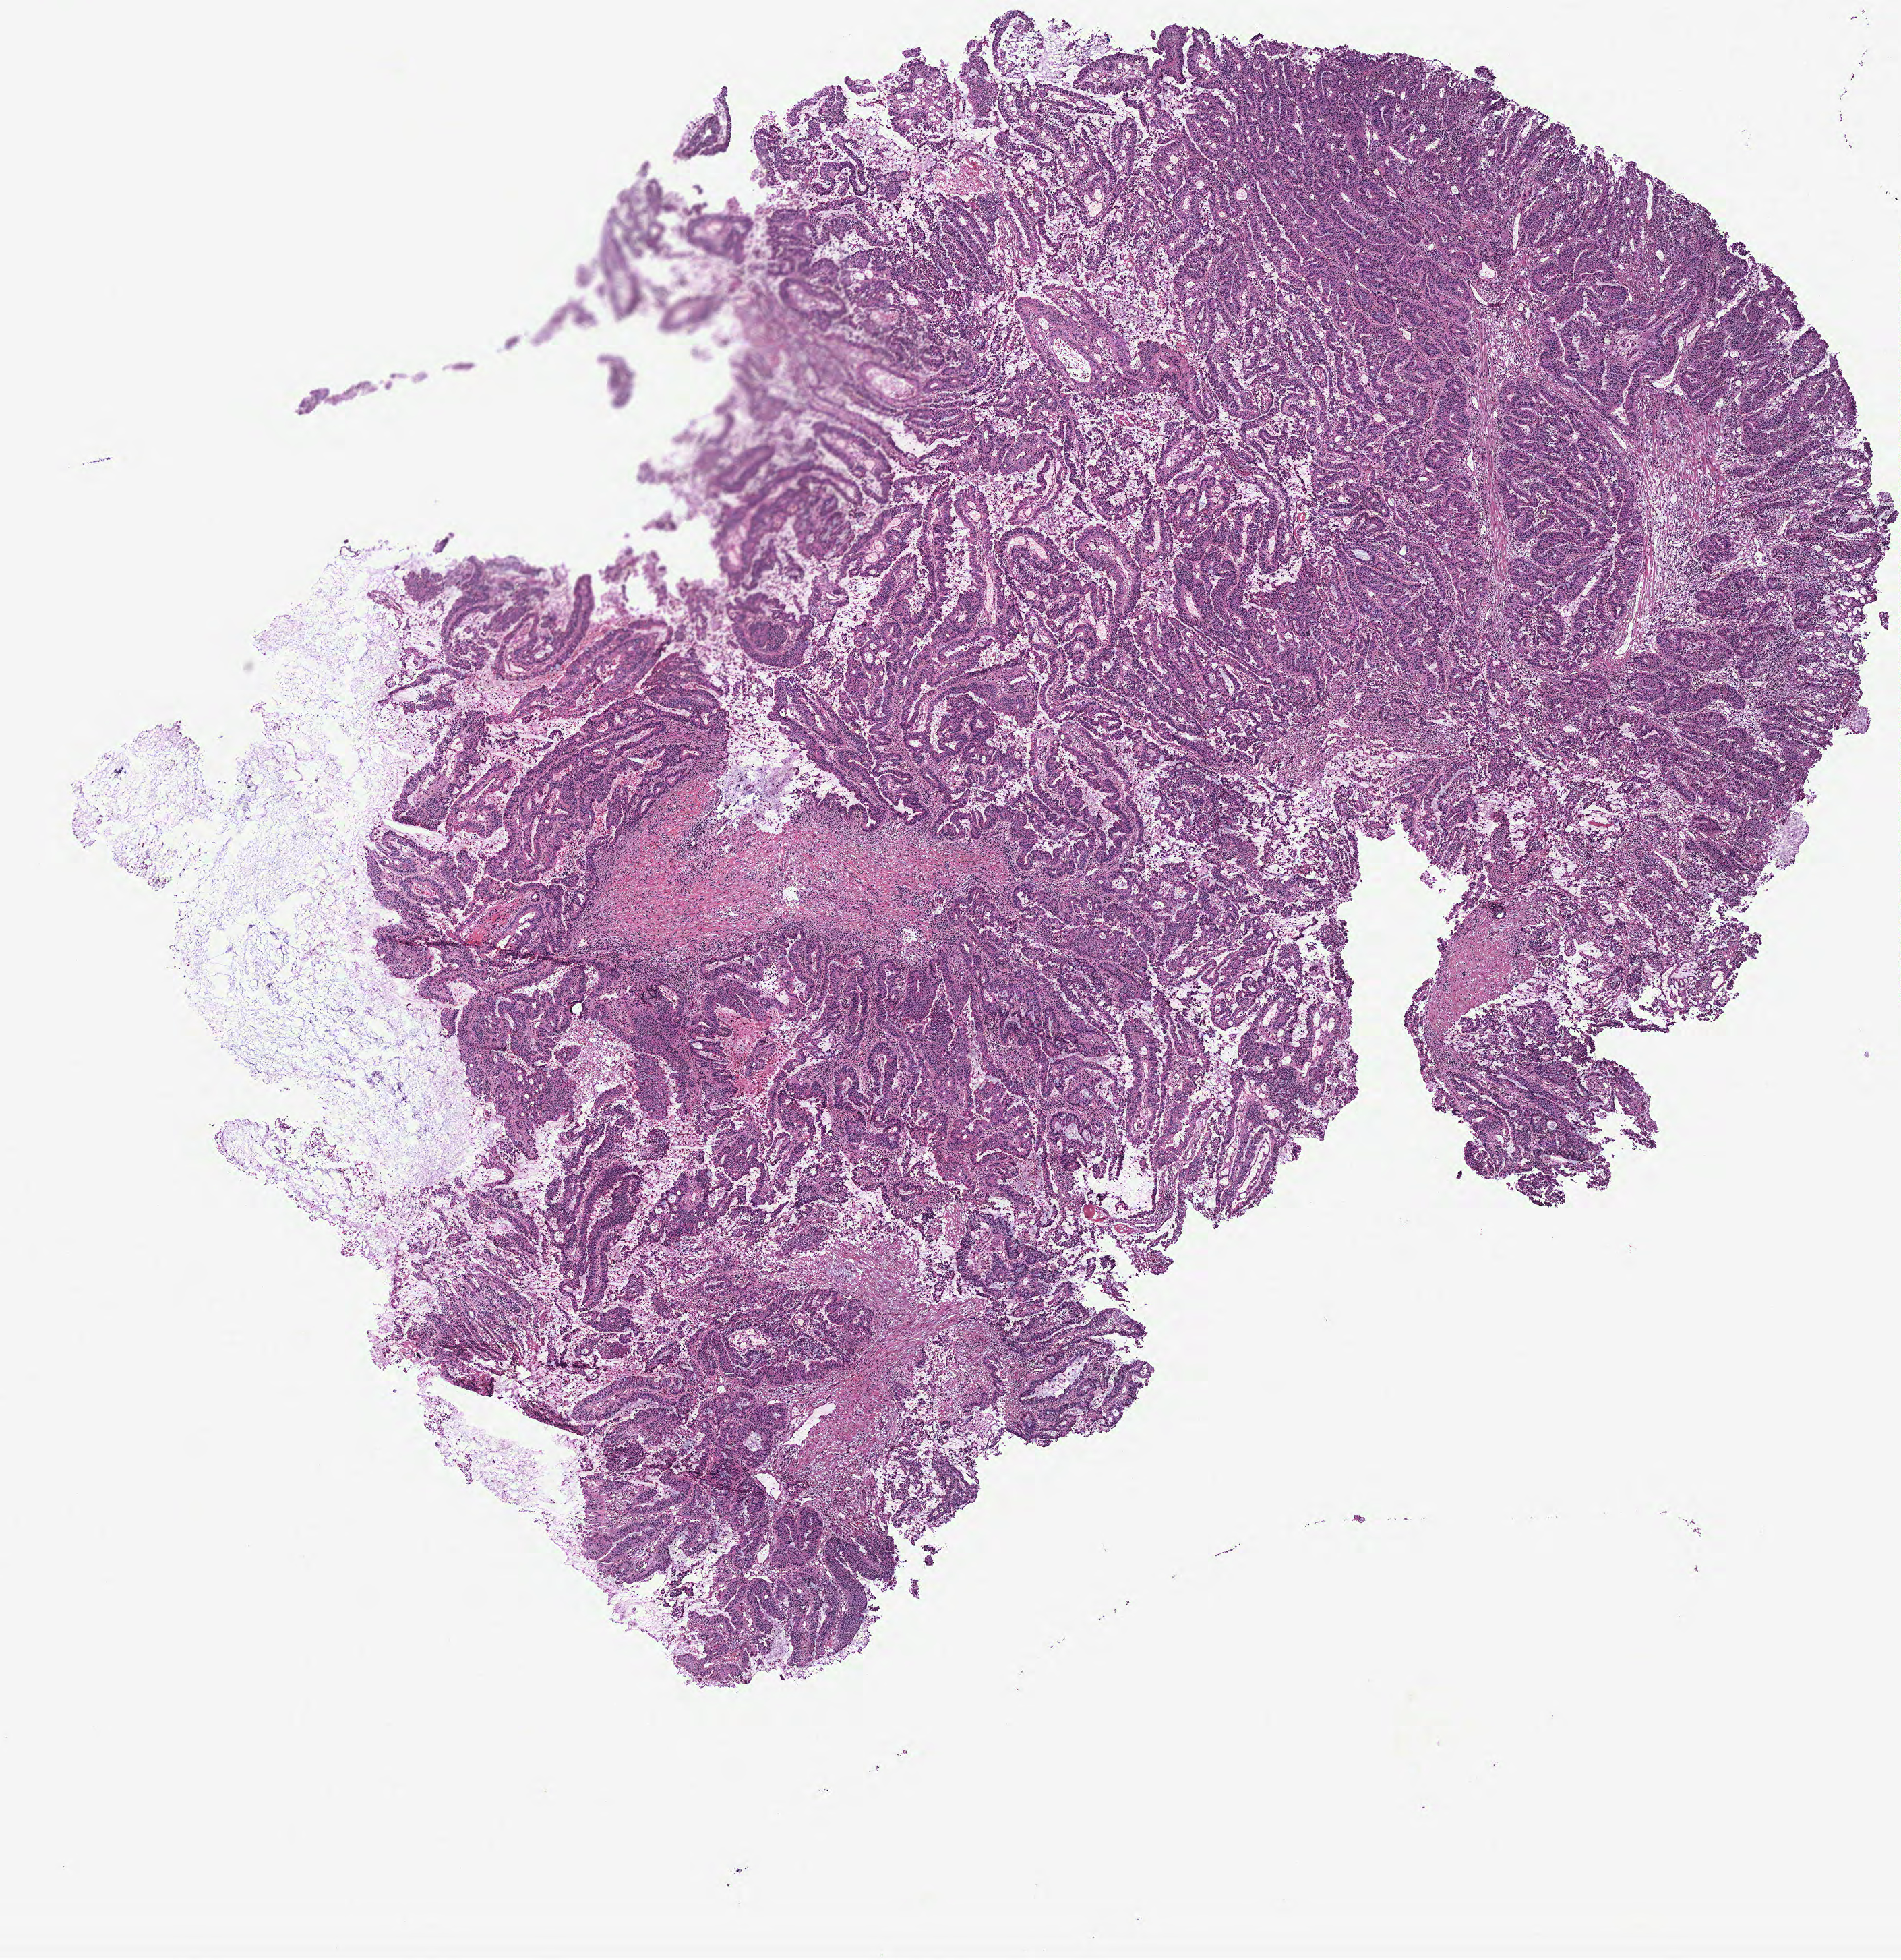
Digitized H&E-stained tissue section (whole slide), shown as a low-resolution overview of the whole scanned area (about 11.3 x 11.6 mm, slide scanned at 40x), colon, tumour tissue. Female, 71 y/o.
Diagnosis: Adenocarcinoma, NOS.